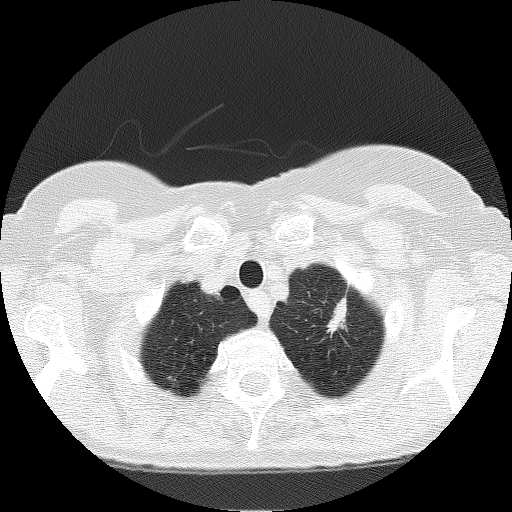
Low-dose screening chest CT, one axial slice; position 153 of 166 along the scan axis; reconstruction kernel FC51; 120 kVp; lung window (W 1500 / L -600 HU); 512 × 512 image matrix.
Structures marked on this image (expert manual segmentation):
- lesion 3 (nodule, upper lobe of left lung): bounding box (x1, y1, x2, y2) in pixels: (327, 299, 347, 333)